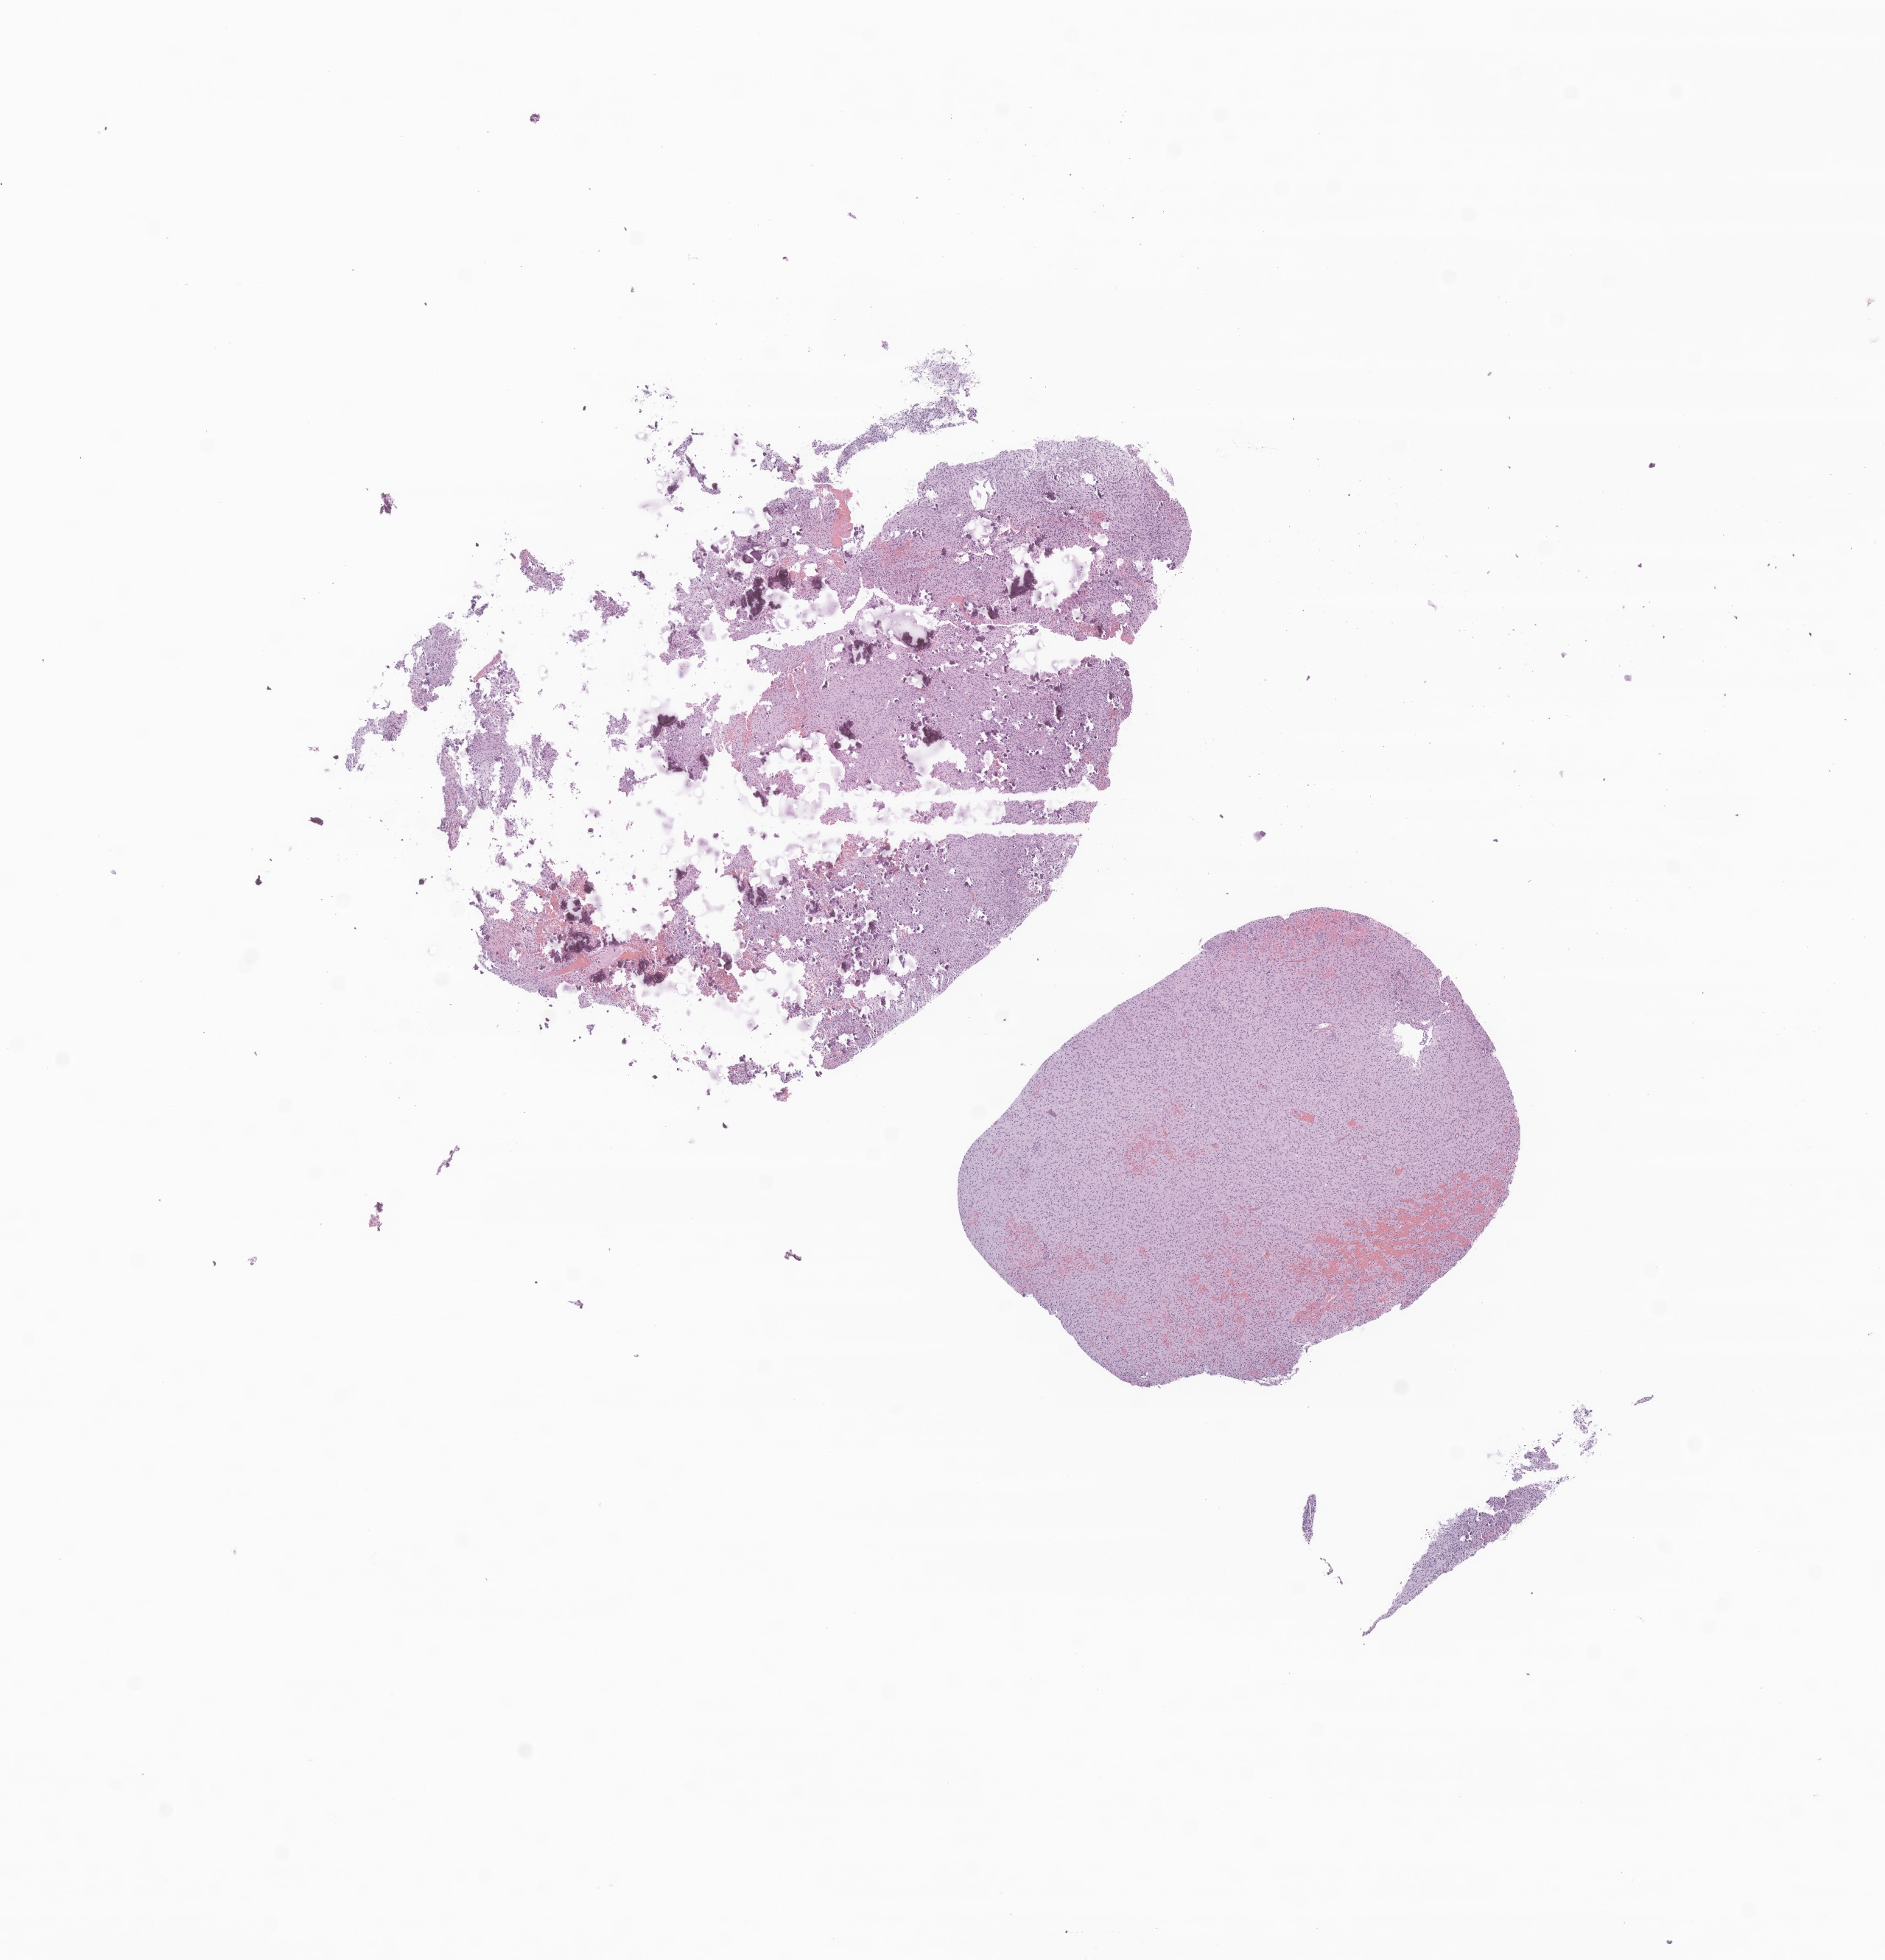
Whole-slide image, H&E stain of tumor tissue from the brain — a low-resolution overview of the entire scanned area, about 10.8 x 11.2 mm; formalin-fixed, paraffin-embedded (FFPE) tissue. Patient: female, age 122 months (10 years 2 months).
Recorded diagnosis: Pleomorphic xanthoastrocytoma, NOS.